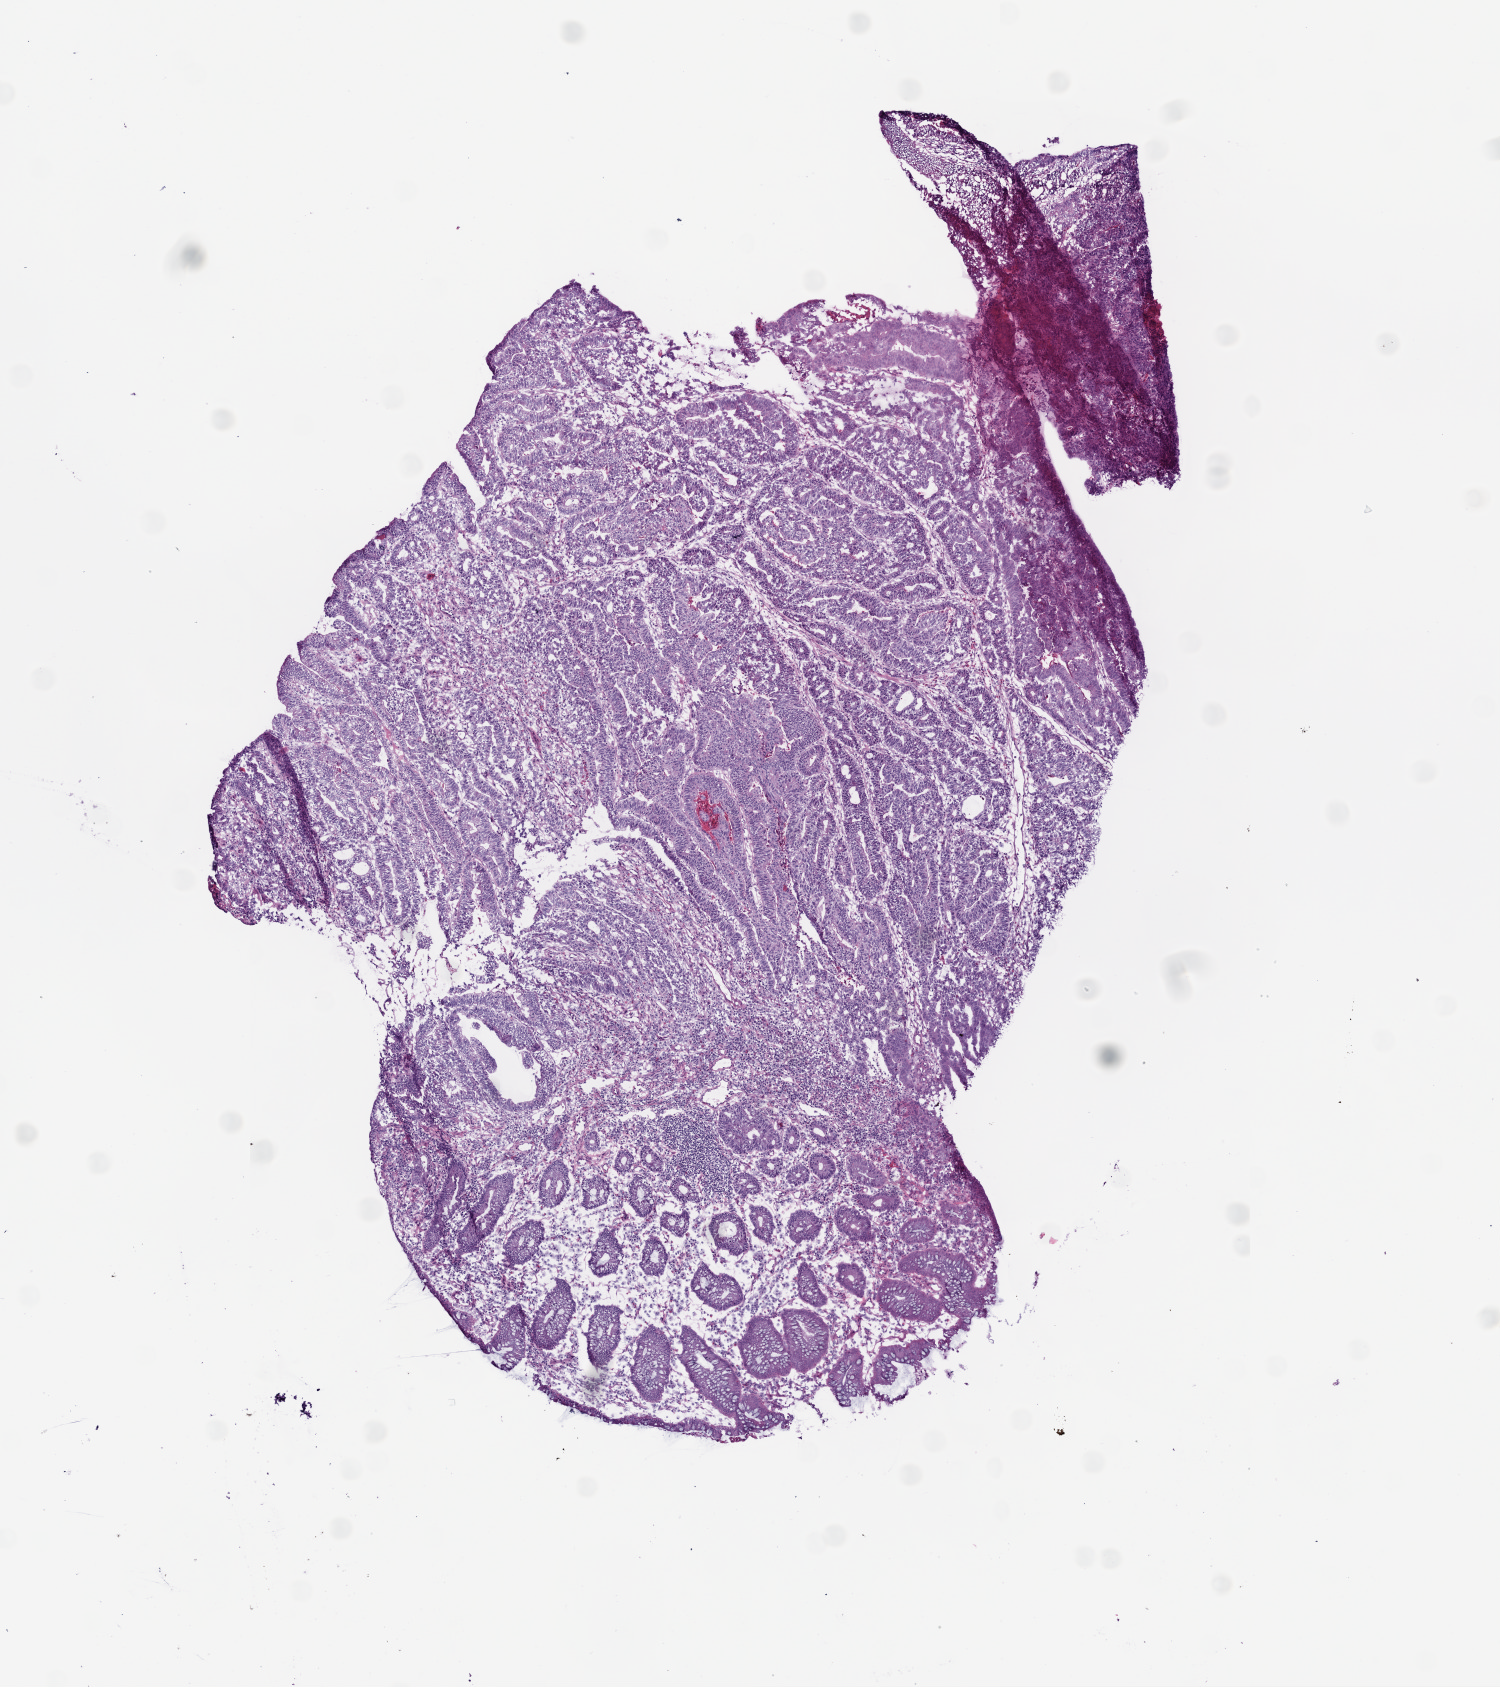
H&E-stained whole-slide image, a low-resolution overview of the entire scanned area, about 6.0 x 6.8 mm (from a 20x scan). Frozen section from the bottom of the tissue portion. Primary tumour sample from the colon. Patient: female, age at initial diagnosis 54 years. Composition of this section per pathologist review: tumour cells 85%, tumour nuclei 75%, normal cells 0%, stromal cells 10%, necrosis 5%.
• histologic diagnosis: Adenocarcinoma, NOS (sigmoid colon)
• lymph nodes positive (case pathology): 0 of 27 examined
• AJCC pathologic stage: II (5th edition)